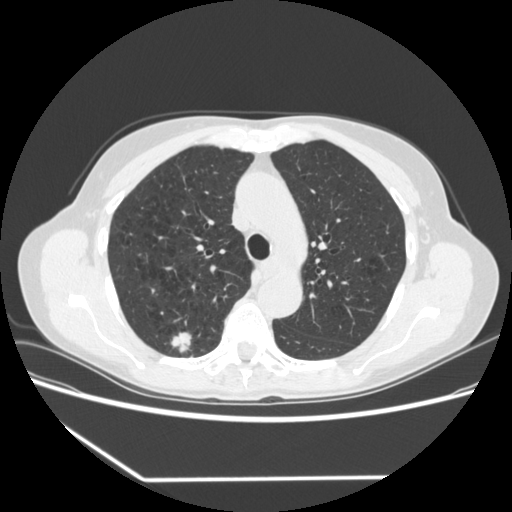
Chest CT (low-dose screening protocol), one axial image; first (baseline) screen; lung window (W 1500 / L -600 HU); 1.25 mm slice thickness; standard (soft-tissue) reconstruction kernel (STANDARD). Female participant, aged 67 years at enrolment. Current smoker at enrolment.
Expert-annotated lung lesion, box from (x=158, y=324) to (x=202, y=362) px. The screening reader recorded 2 non-calcified nodules or masses ≥4 mm on this exam (right upper lobe, right lower lobe); which of them this box marks is not recorded. Official screen result: positive, change unspecified: nodule(s) >= 4 mm or enlarging nodule(s), mass(es), or other non-specific abnormalities suspicious for lung cancer. Participant outcome: lung cancer diagnosed 29 days after this screen — adenocarcinoma, NOS, right upper lobe, moderately differentiated (G2), stage IA (AJCC 6th edition), 24 mm at pathology.